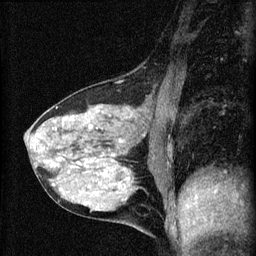
Breast MRI (dynamic contrast-enhanced), one sagittal slice. Position 24 of 60 along the scan axis. Dynamic contrast-enhanced series, image 2 of 4 at this slice position (ordered by acquisition). 1.5 T. TE 4.2 ms, TR 8.2 ms. 2 mm slice thickness. 256 × 256 image matrix, field of view 180 × 180 mm. Female patient, age 41 years.
Outlined on this slice (semi-automatic segmentation, software-assisted and operator-edited):
- analysis volume of interest (the breast-tissue region the enhancement analysis was run in; not a lesion): bounding box (x1, y1, x2, y2) in pixels: (25, 91, 166, 210)
- tumour enhancement mask (voxels above the 70 % enhancement threshold inside the analysis volume of interest): (33, 127, 98, 185)